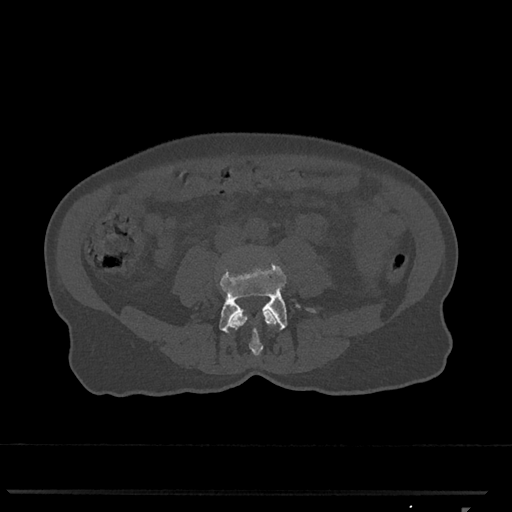
CT including the spine, one axial slice; position 231 of 793 along the scan axis; reconstruction kernel Br40s/3; 120 kVp; bone window (W 1800 / L 400 HU); 0.5 mm slice thickness; 512 × 512 image matrix, field of view 380 × 380 mm. Patient: female, 62 years. From the clinical record (not read from this slice): primary cancer: renal.
Outlined on this slice (semi-automatically segmented with operator editing):
- L3 vertebra: bounding box <230,310,276,356> (left, top, right, bottom; pixels)
- L4 vertebra: <219,263,315,333>